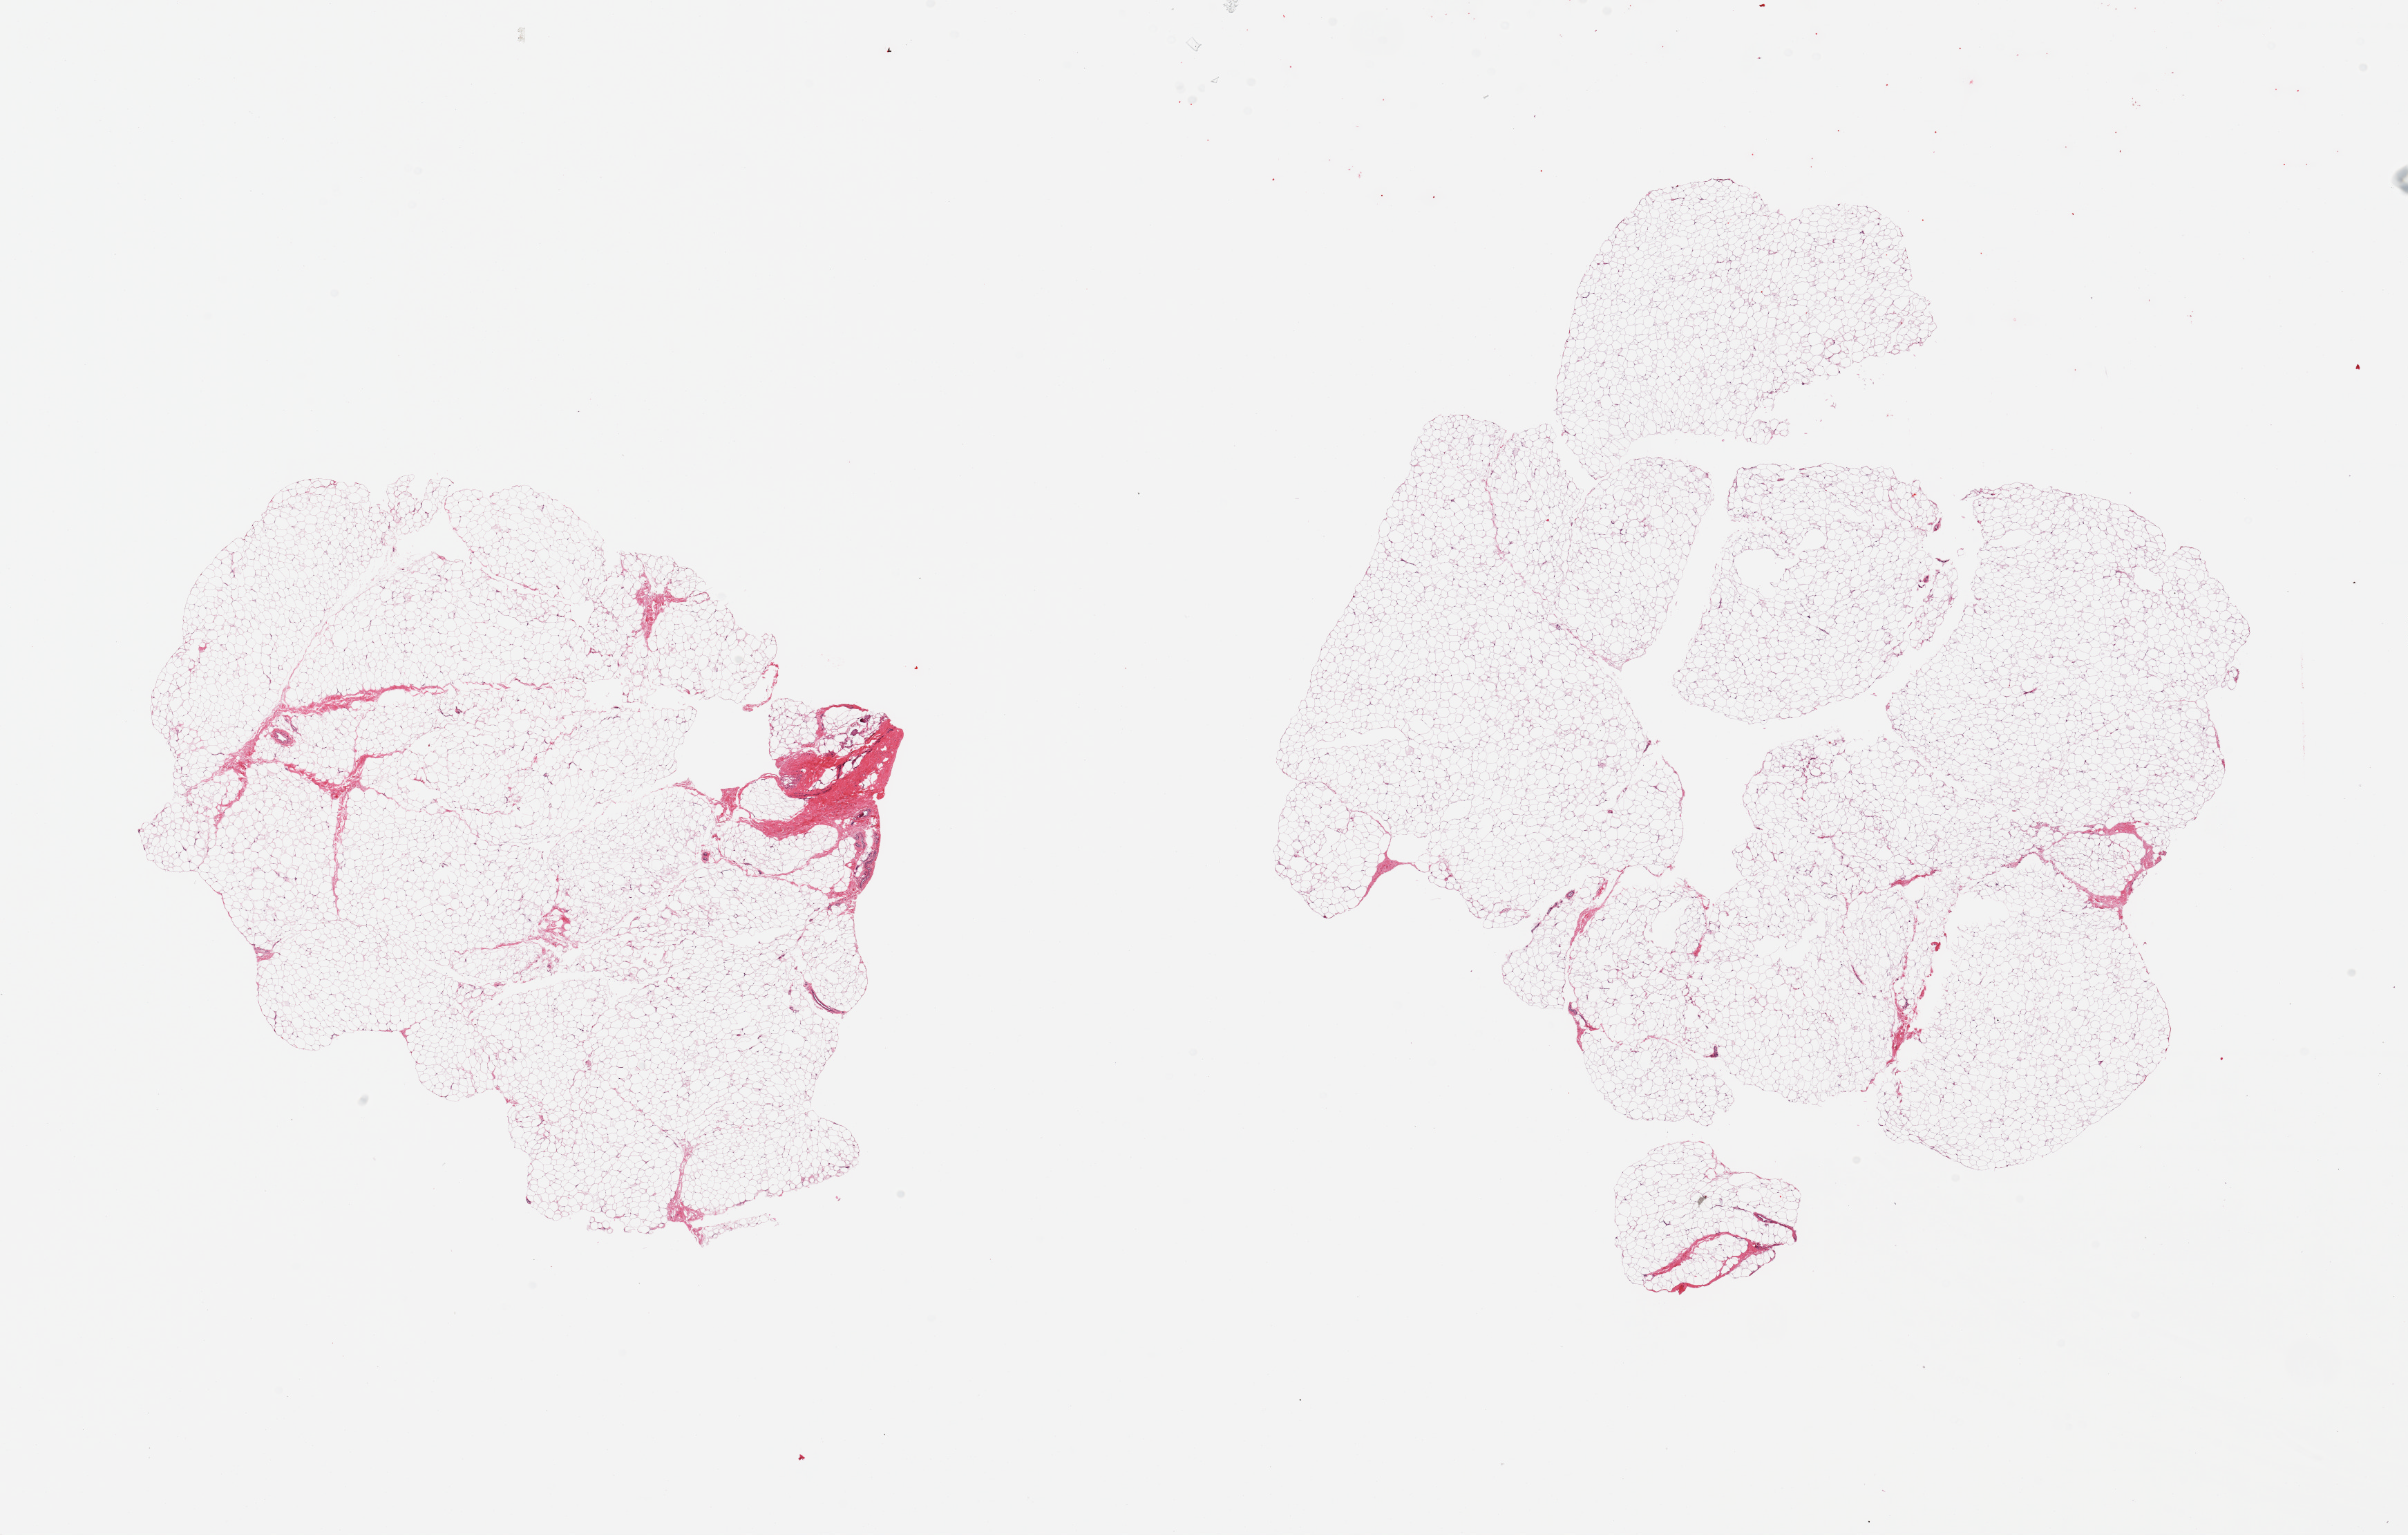
Whole-slide image, hematoxylin and eosin (H&E) stain, brightfield — a low-resolution overview of the entire scanned area, about 27.6 x 17.6 mm, PAXgene-fixed paraffin-embedded (PFPE) section, section of breast (target tissue), tissue donor sample. Donor: male.
- reviewer comment on this tissue sample: 2 pieces; predominantly fat, 1 piece has small portion fibrocollagenous stroma (<10%)